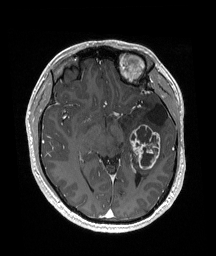
Brain MRI from a brain-tumour surgery series, one axial slice; position 100 of 192 along the scan axis; T1-weighted post-contrast; 1 mm slice thickness; 216 × 256 image matrix, field of view 211 × 250 mm. From the clinical record (not read from this slice): histopathology: Glioneuronal tumor; WHO grade: 2; tumour location: Left Superior Temporal Gyrus.
Structures marked on this image (manually delineated by an expert):
- previous resection cavity: bounding box [x1, y1, x2, y2] px = [148, 104, 168, 126]
- tumour: [129, 124, 160, 169]